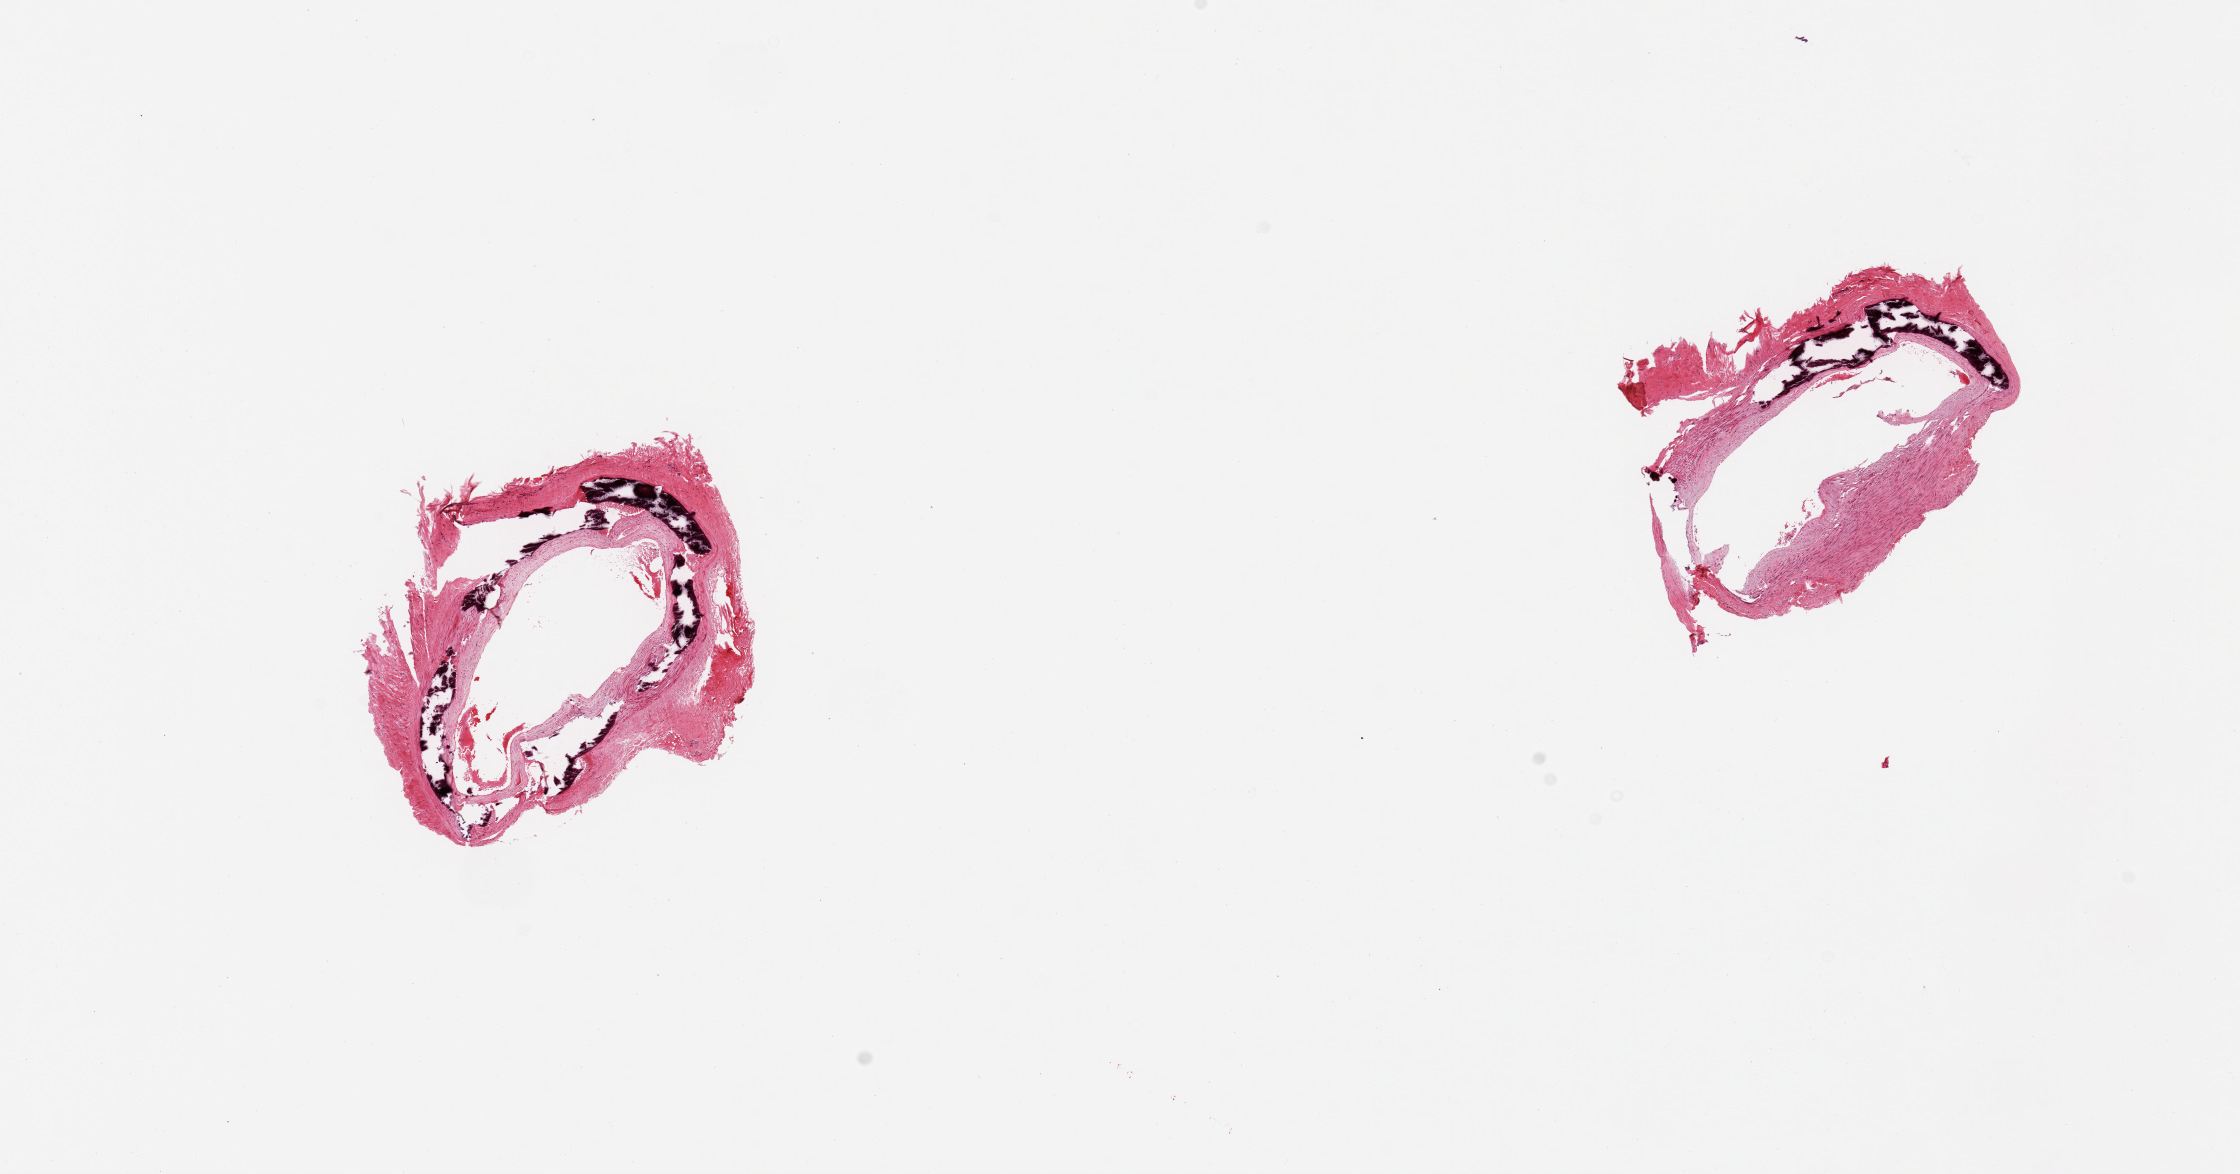
Digitized hematoxylin and eosin (H&E)-stained section, brightfield — shown as a low-resolution overview of the whole scanned area (about 17.7 x 9.3 mm), PAXgene-fixed paraffin-embedded (PFPE) section, section of tibial artery (target tissue), donor tissue sample. Female donor.
Pathologist's review note for this sample: 2 pieces, no atherosis/adherant fat; prominent Monckeberg sclerosis.